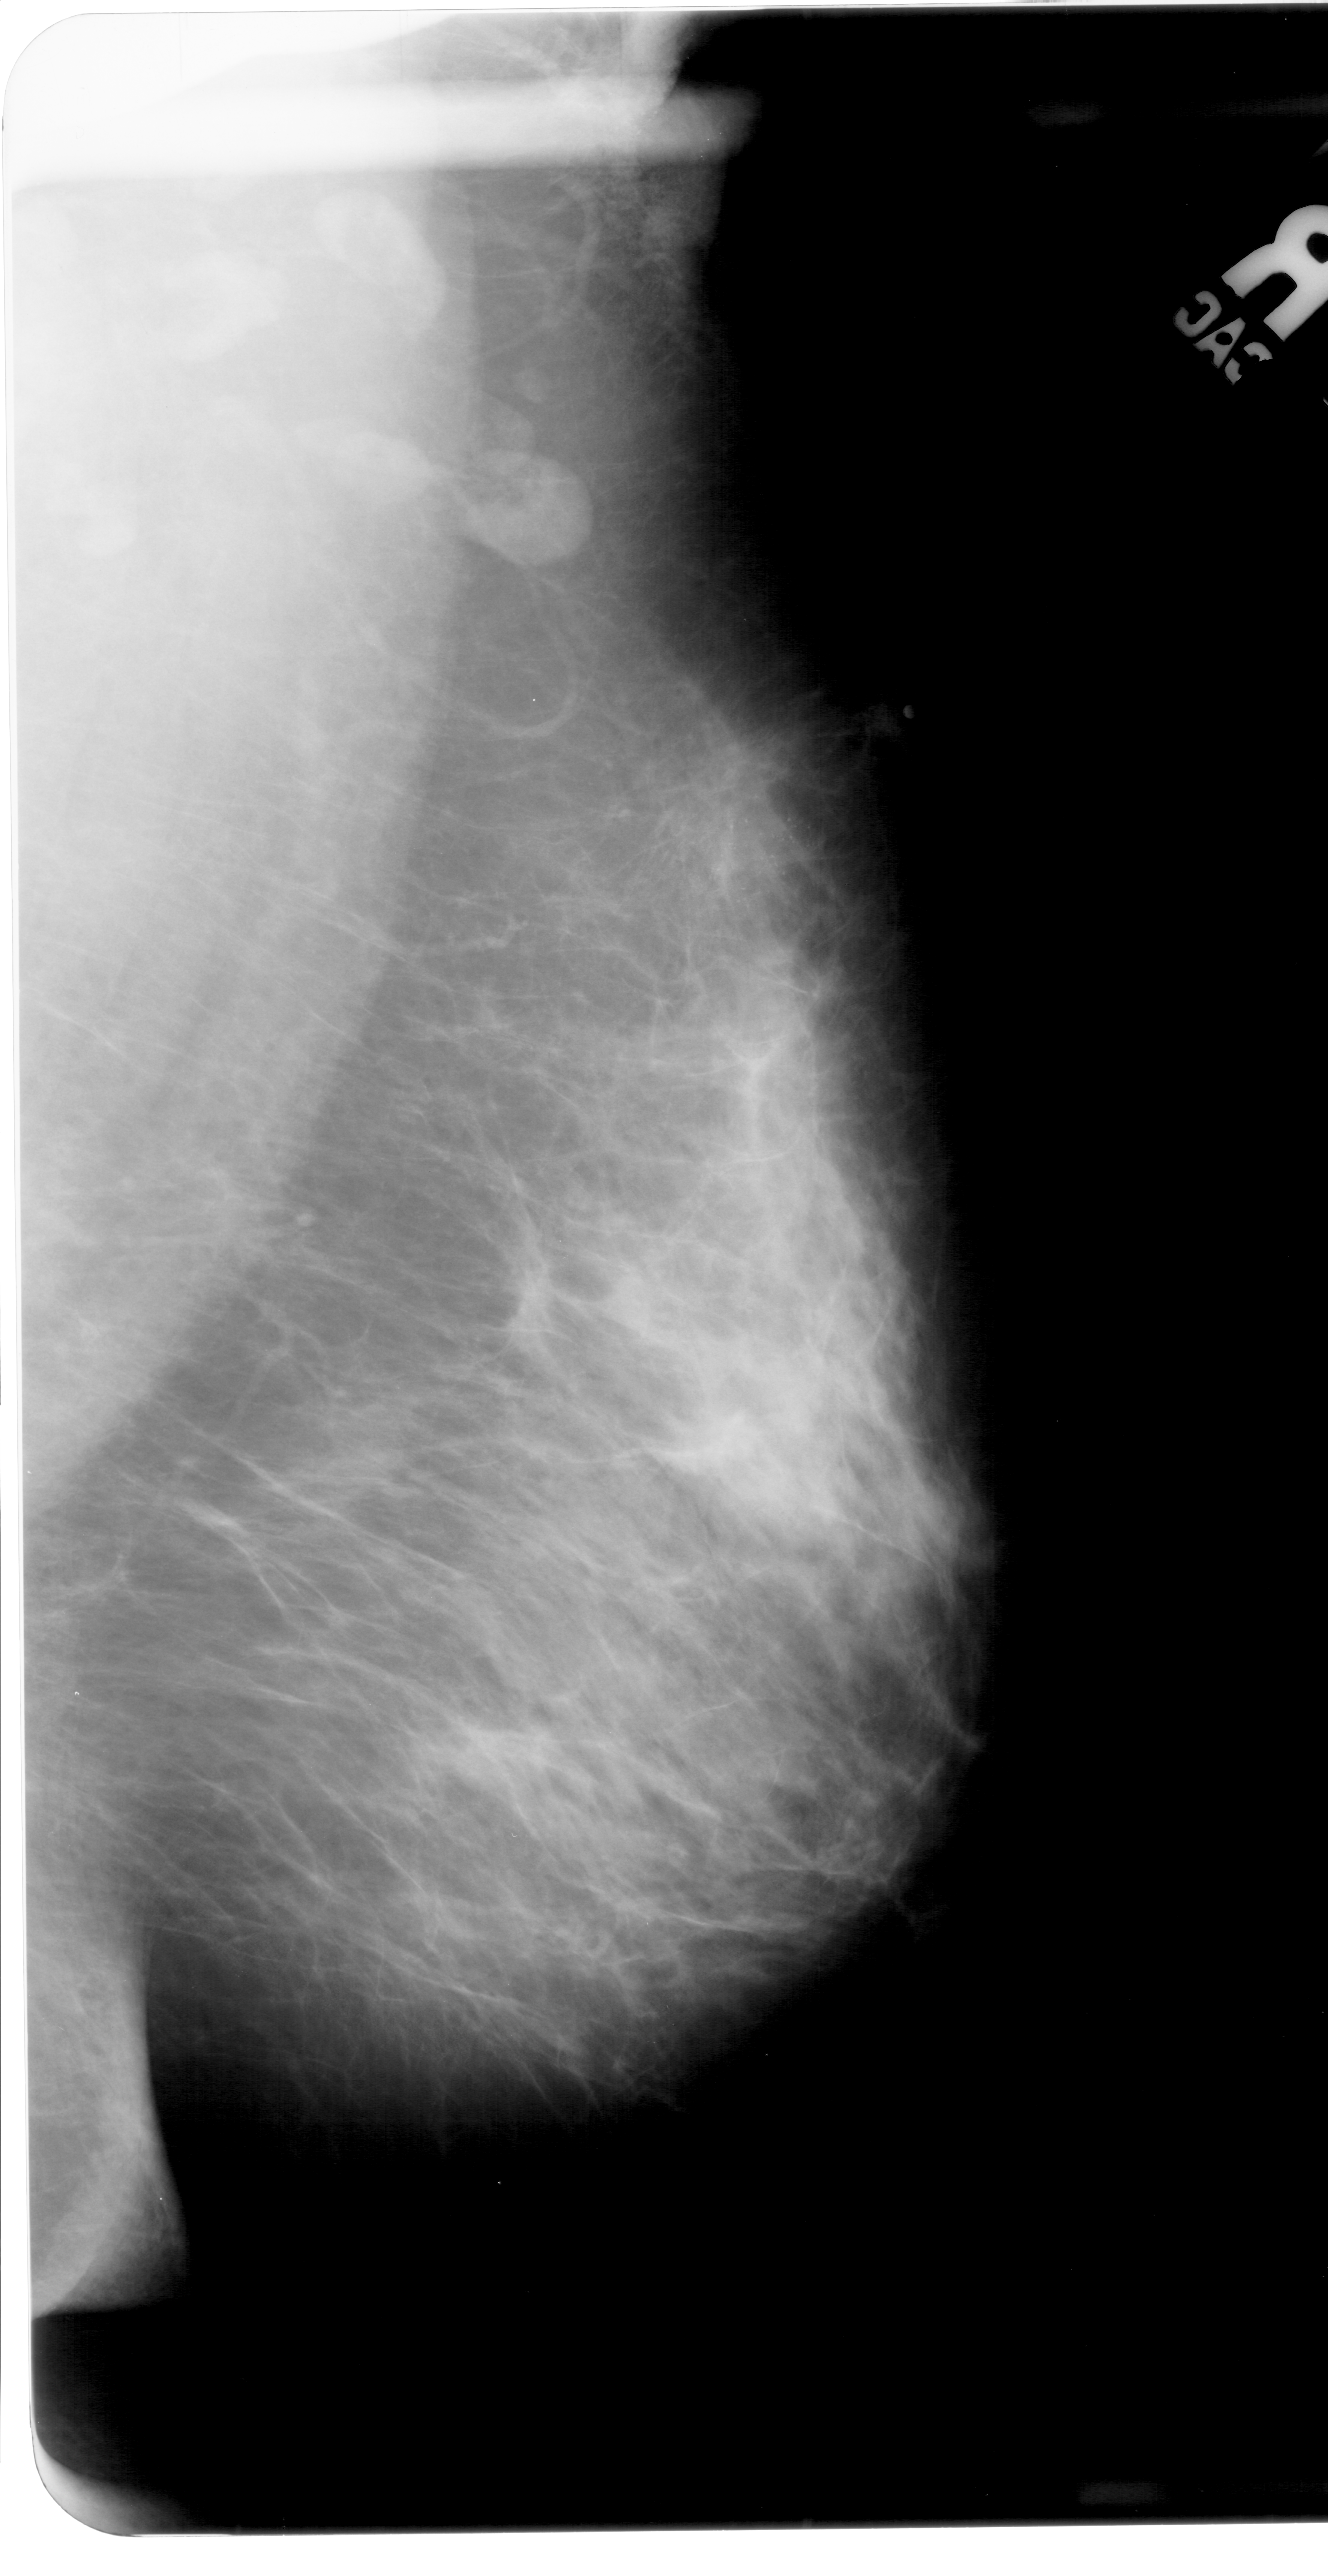
Mammogram (digitized film); right breast; MLO view; BI-RADS breast density category 3 (scale 1–4); 1328 × 2576 image matrix.
Expert-marked regions of interest on this image (one box per marked abnormality):
- calcifications, morphology pleomorphic, distribution clustered; BI-RADS assessment category 4; pathology result (as recorded, not read from the image): malignant: box from (x=679, y=781) to (x=848, y=971) px